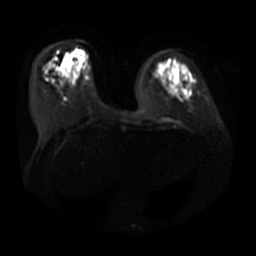
Breast MRI, one axial slice; position 11 of 31 along the scan axis; diffusion-weighted series; image 2 of 4 stored at this slice position (different b-values; order by instance number); 3 T; 5 mm slice thickness; 256 × 256 image matrix. Female patient.
Structures marked on this image (expert manual segmentation):
- tumour on diffusion-weighted imaging: bounding box (x1, y1, x2, y2) in pixels: (63, 57, 70, 66)